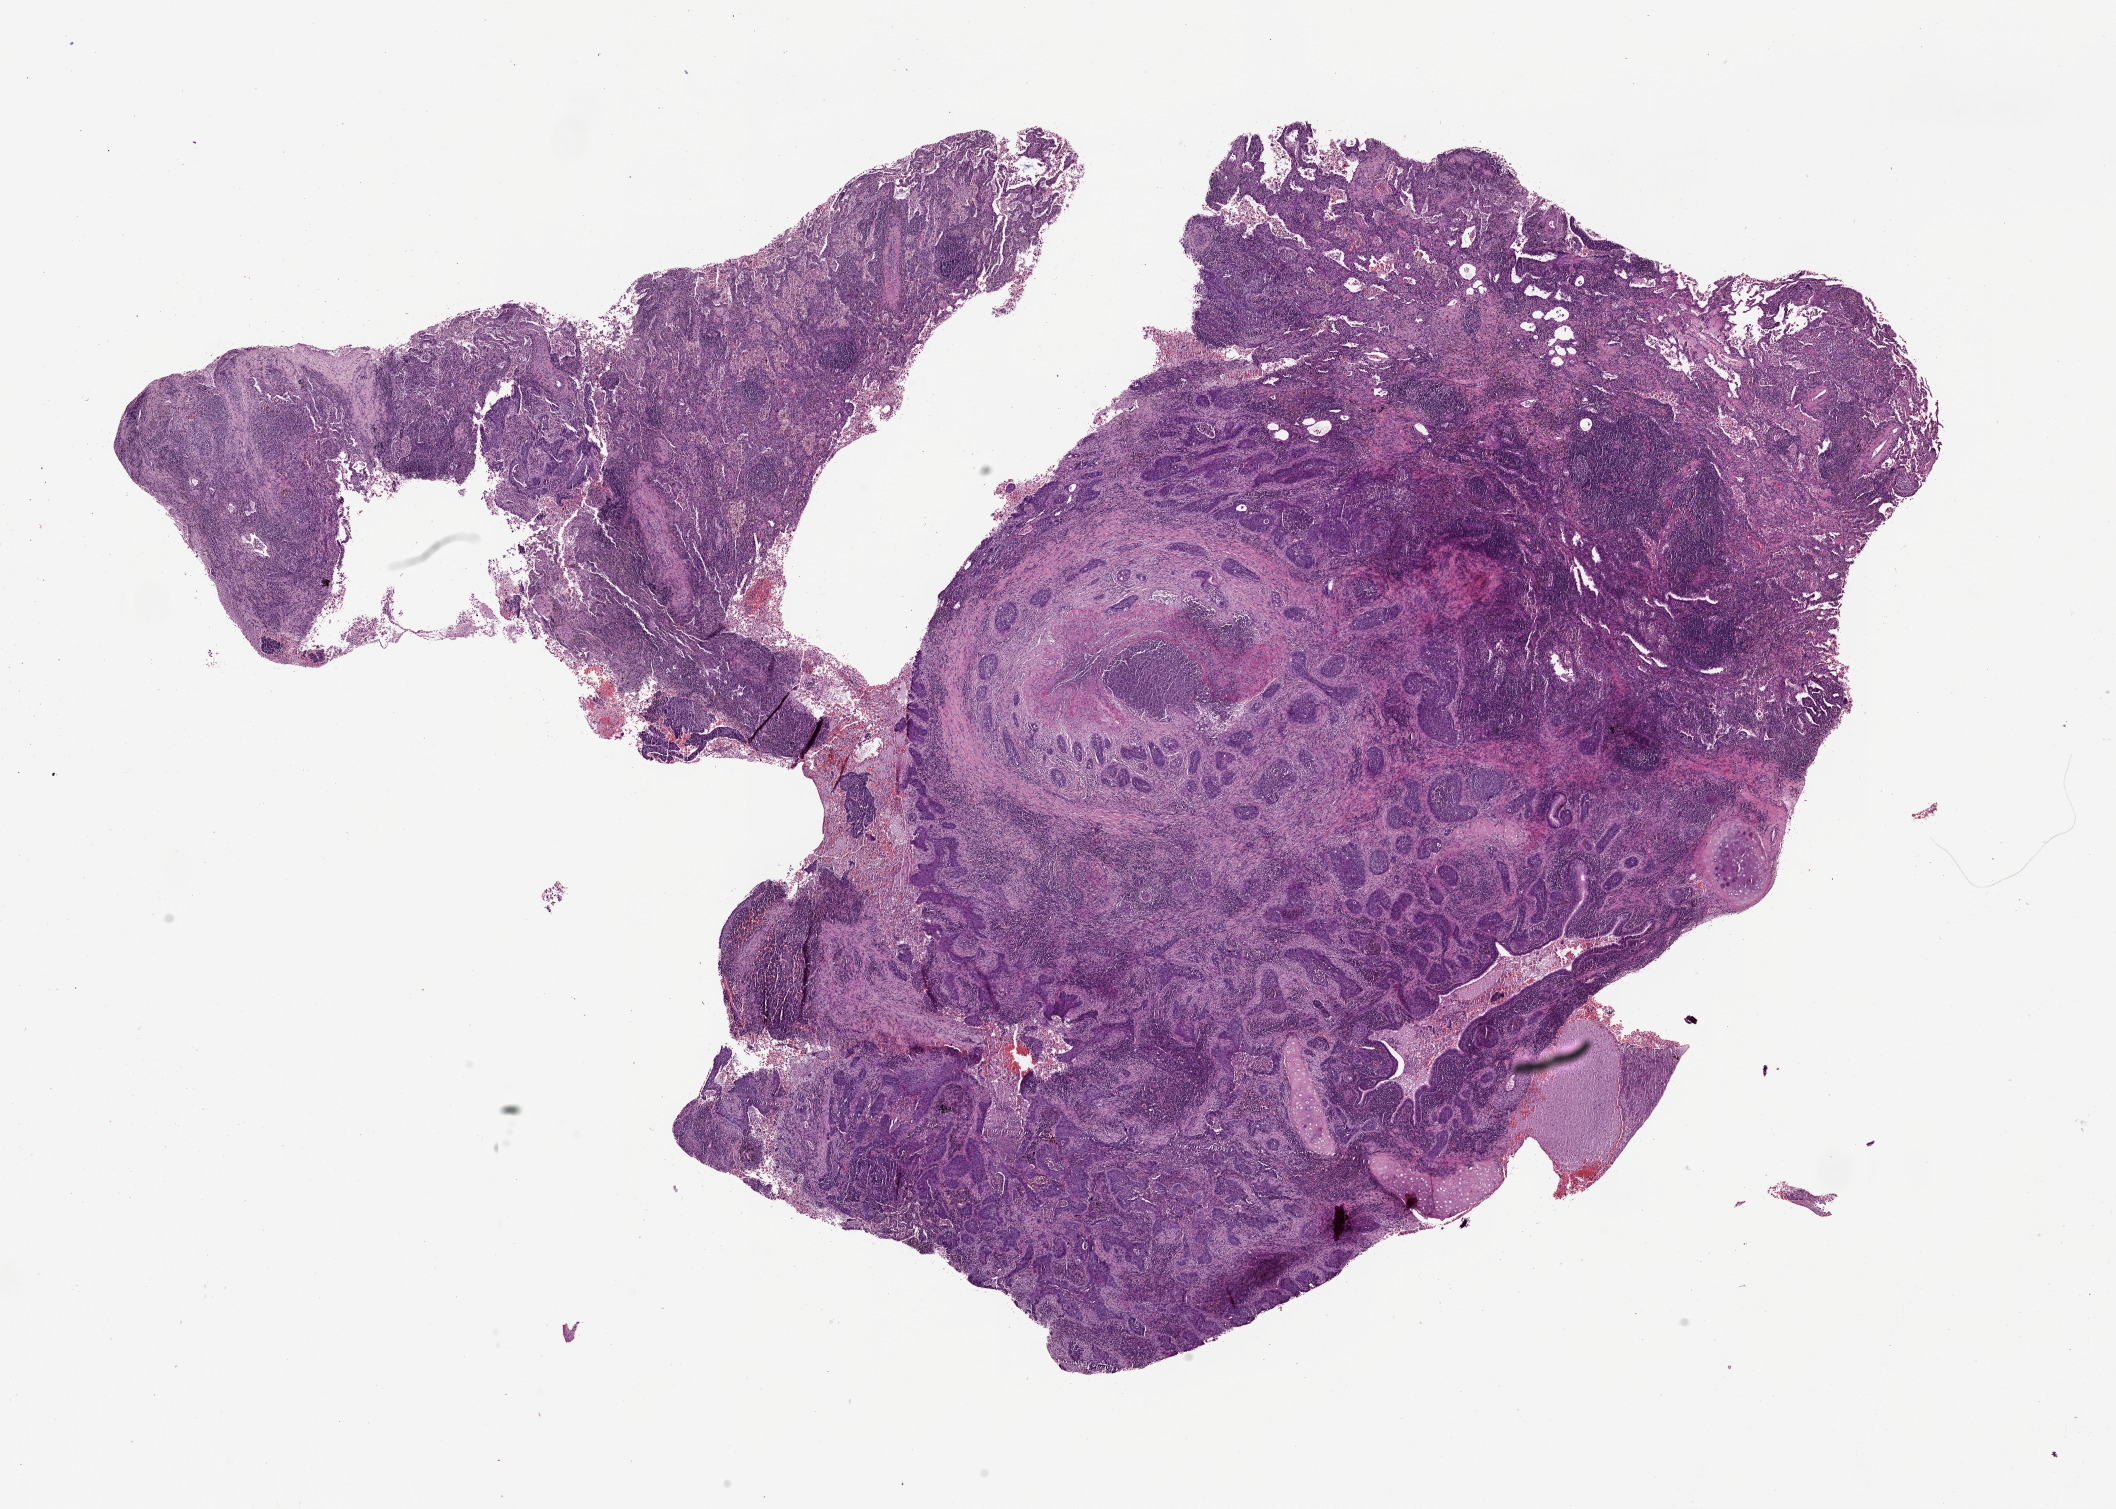
Whole-slide histology image, H&E-stained — low-resolution overview of the scanned area, about 17.0 x 12.1 mm. Tumour tissue sample, lung. Male, 59 y/o.
Patient diagnosis (cohort enrolment): squamous cell carcinoma (lung).